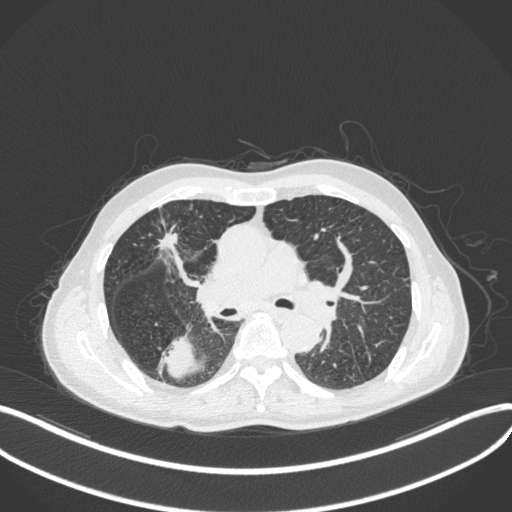
Chest CT, one axial slice. Slice 271 of 423 in the series (ordered by position). 120 kVp. Lung window (W 1500 / L -600 HU). 1 mm slice thickness. 512 × 512 image matrix, field of view 400 × 400 mm. Patient: male, 79 years. Case-level facts recorded for this patient, not image findings: clinical TNM (as recorded): T3 N0 M0.
Outlined on this slice (rectangle marked by the reading radiologist):
- lung tumour (recorded histology: adenocarcinoma): bounding box (x1, y1, x2, y2) in pixels: (155, 331, 202, 384)